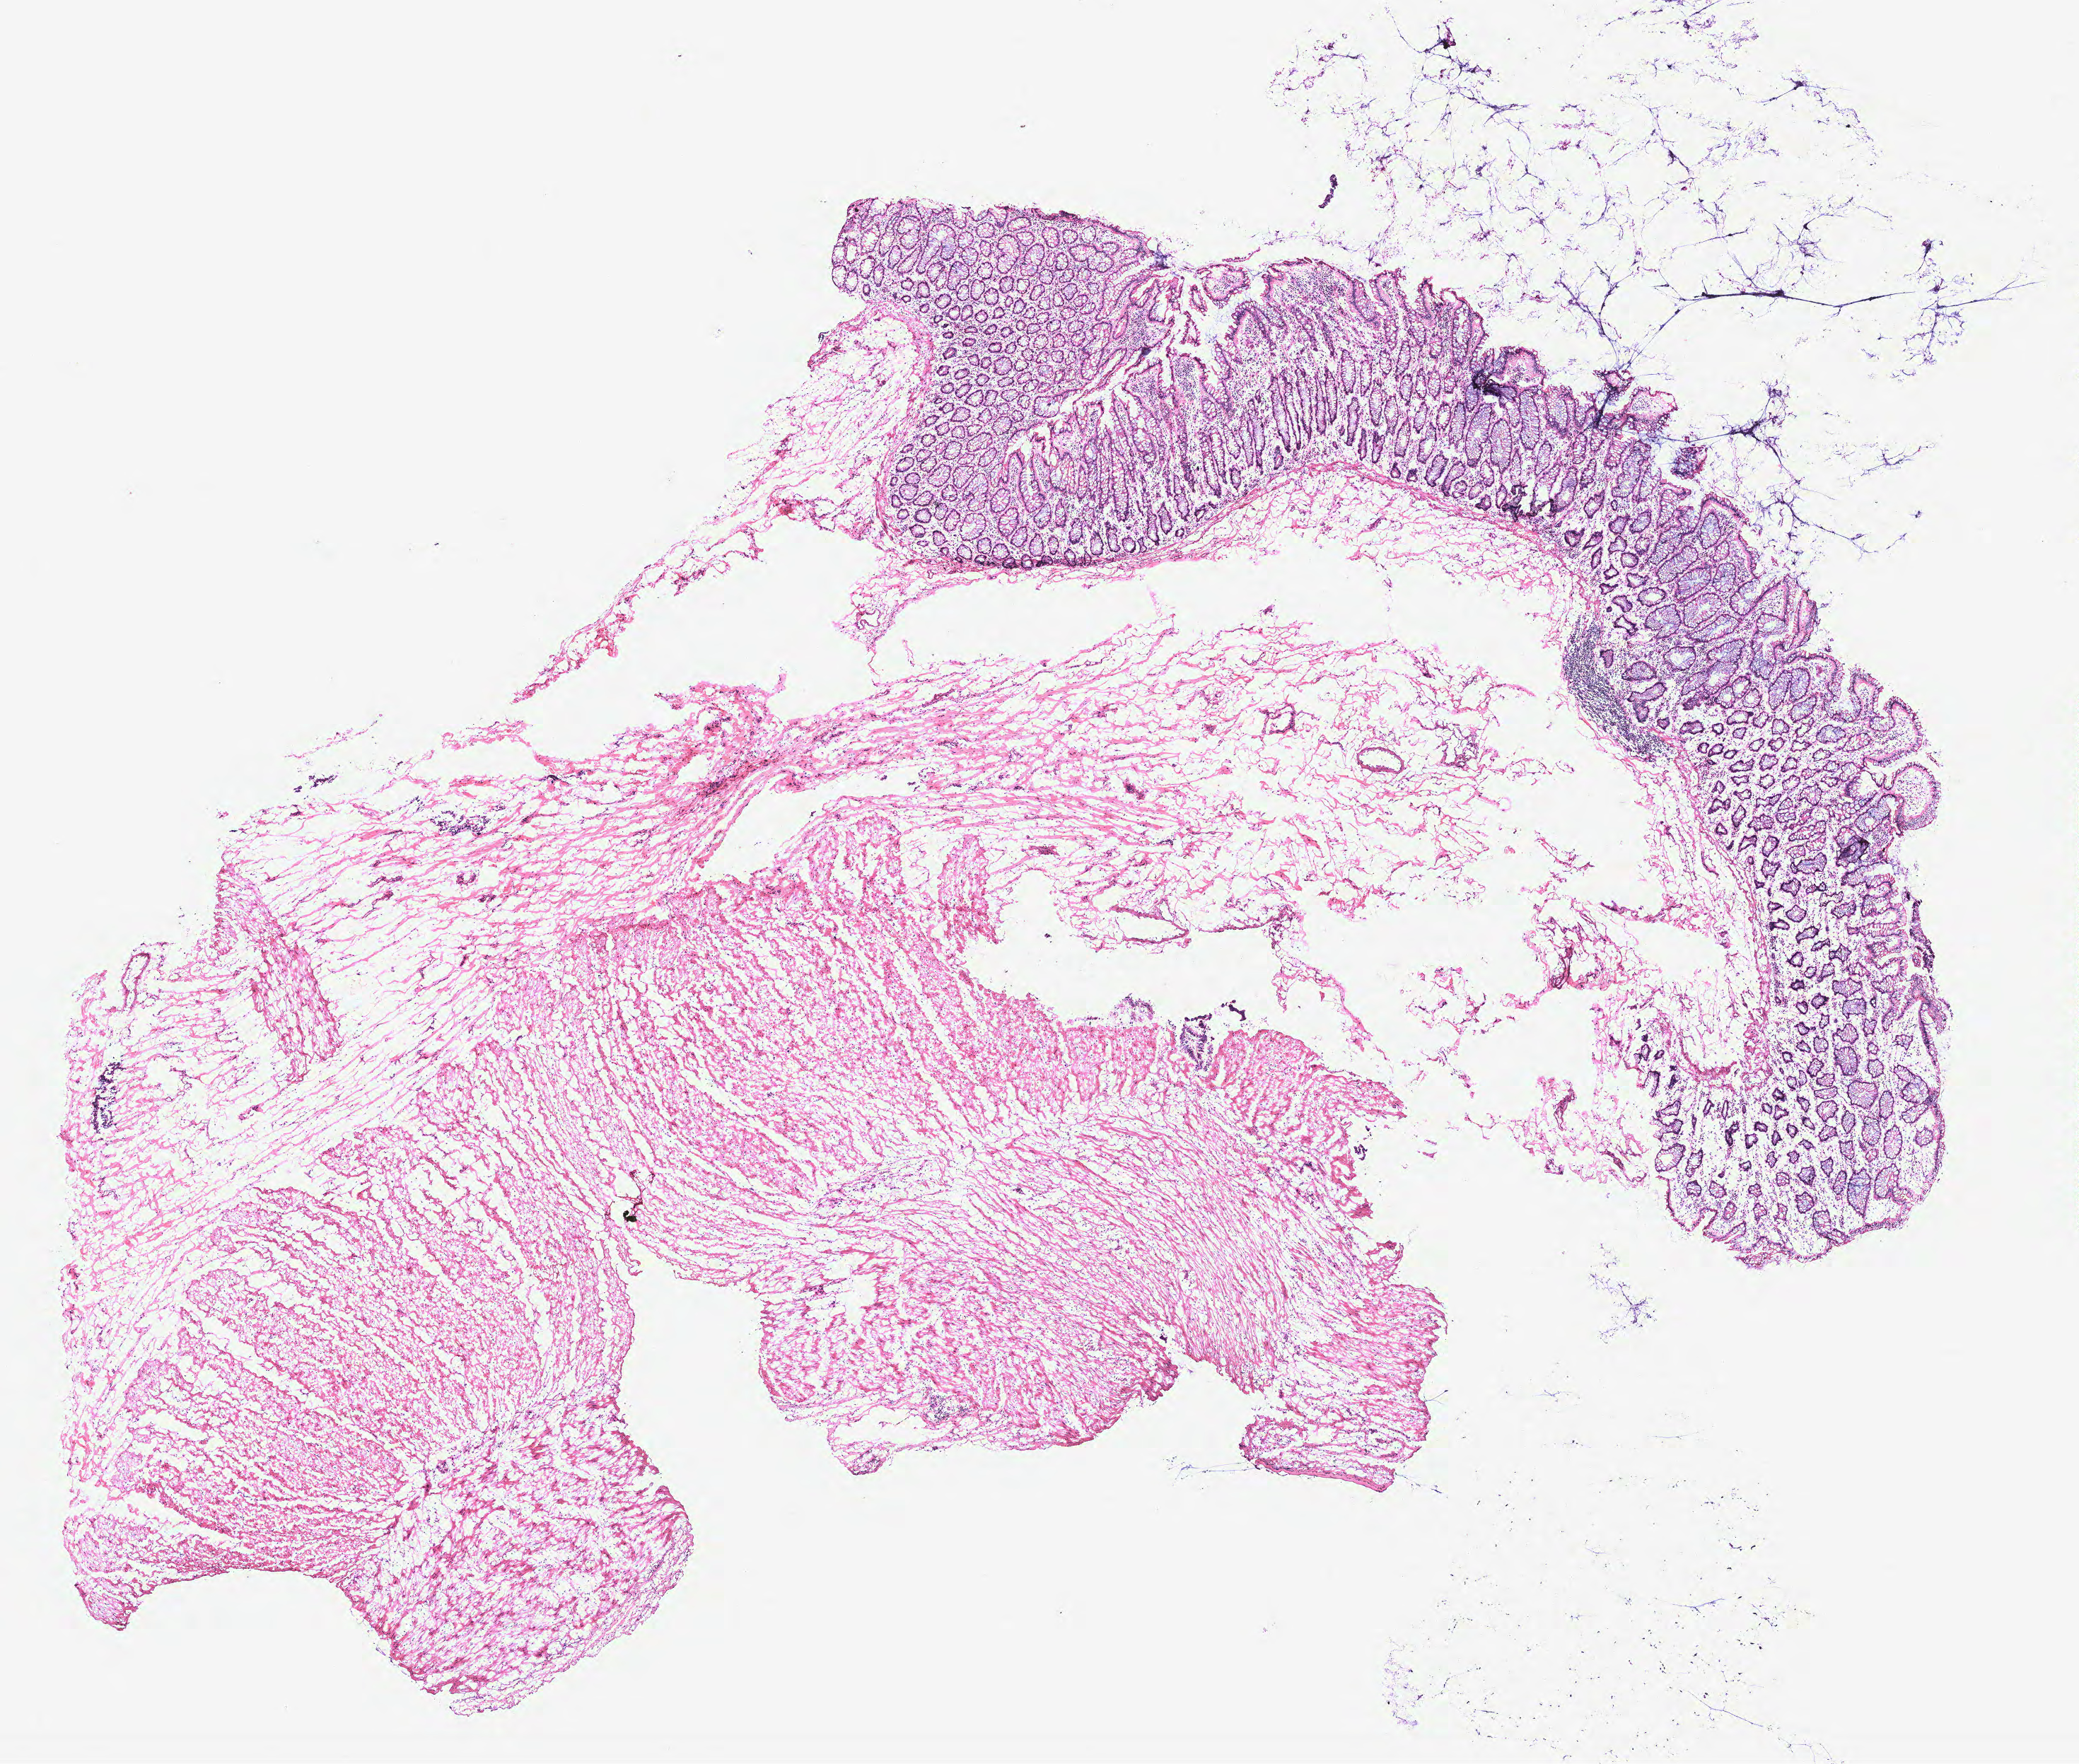
Hematoxylin and eosin (H&E) stained whole-slide image, a low-resolution overview of the entire scanned area, about 11.8 x 10.0 mm (from a 40x scan). Colon, tissue type not recorded.
Patient diagnosis (cohort enrolment): colon cancer (colon).